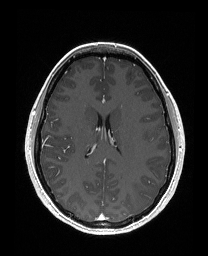
Brain MRI from a brain-tumour surgery series, one axial slice; position 98 of 176 along the scan axis; T1-weighted post-contrast; 1 mm slice thickness; 208 × 256 image matrix, field of view 203 × 250 mm. From the clinical record (not read from this slice): histopathology: Astrocytoma; WHO grade: 3; IDH mutation: yes; tumour location: Left Frontal.
Structures marked on this image (manually delineated by an expert):
- tumour: bounding box (x1, y1, x2, y2) in pixels: (140, 130, 149, 140)